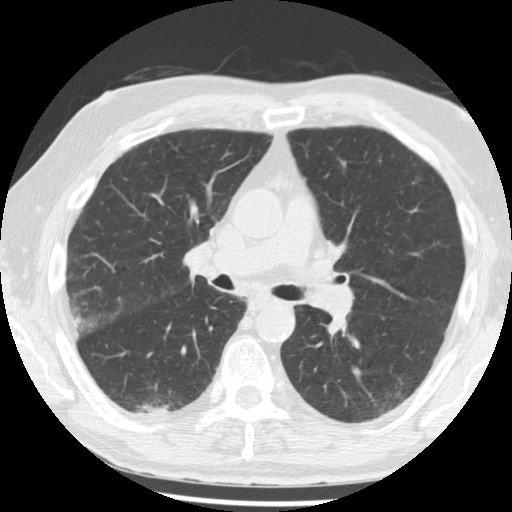
Low-dose screening chest CT, one axial slice. Slice 121 of 221 in the series (ordered by position). Reconstruction kernel STANDARD. 120 kVp. Lung window (W 1500 / L -600 HU). 2.5 mm slice thickness. 512 × 512 image matrix, field of view 350 × 350 mm.
Annotated regions visible in this slice (outlined manually by an expert reader):
- lesion 1 (tumor, lower lobe of right lung): bounding box <140,405,176,415> (left, top, right, bottom; pixels)